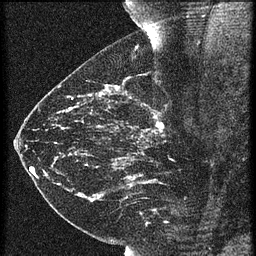
Breast MRI (dynamic contrast-enhanced), one sagittal slice; slice 32 of 60 in the series (ordered by position); 3 images stored at this slice position (order not interpretable as contrast timing); 1.5 T; TE 4.2 ms, TR 21.3 ms; 1.5 mm slice thickness; 256 × 256 image matrix, field of view 180 × 180 mm. Patient: female, 43 years. From the clinical record (not read from this slice): setting: breast cancer imaged before/during neoadjuvant chemotherapy; receptor status: HER2-positive.
Annotated regions visible in this slice (semi-automatic segmentation, software-assisted and operator-edited):
- analysis volume of interest (the breast-tissue region the enhancement analysis was run in; not a lesion): bounding box (x1, y1, x2, y2) in pixels: (119, 114, 189, 173)
- tumour enhancement mask (voxels above the 90 % enhancement threshold inside the analysis volume of interest): (155, 116, 164, 131)